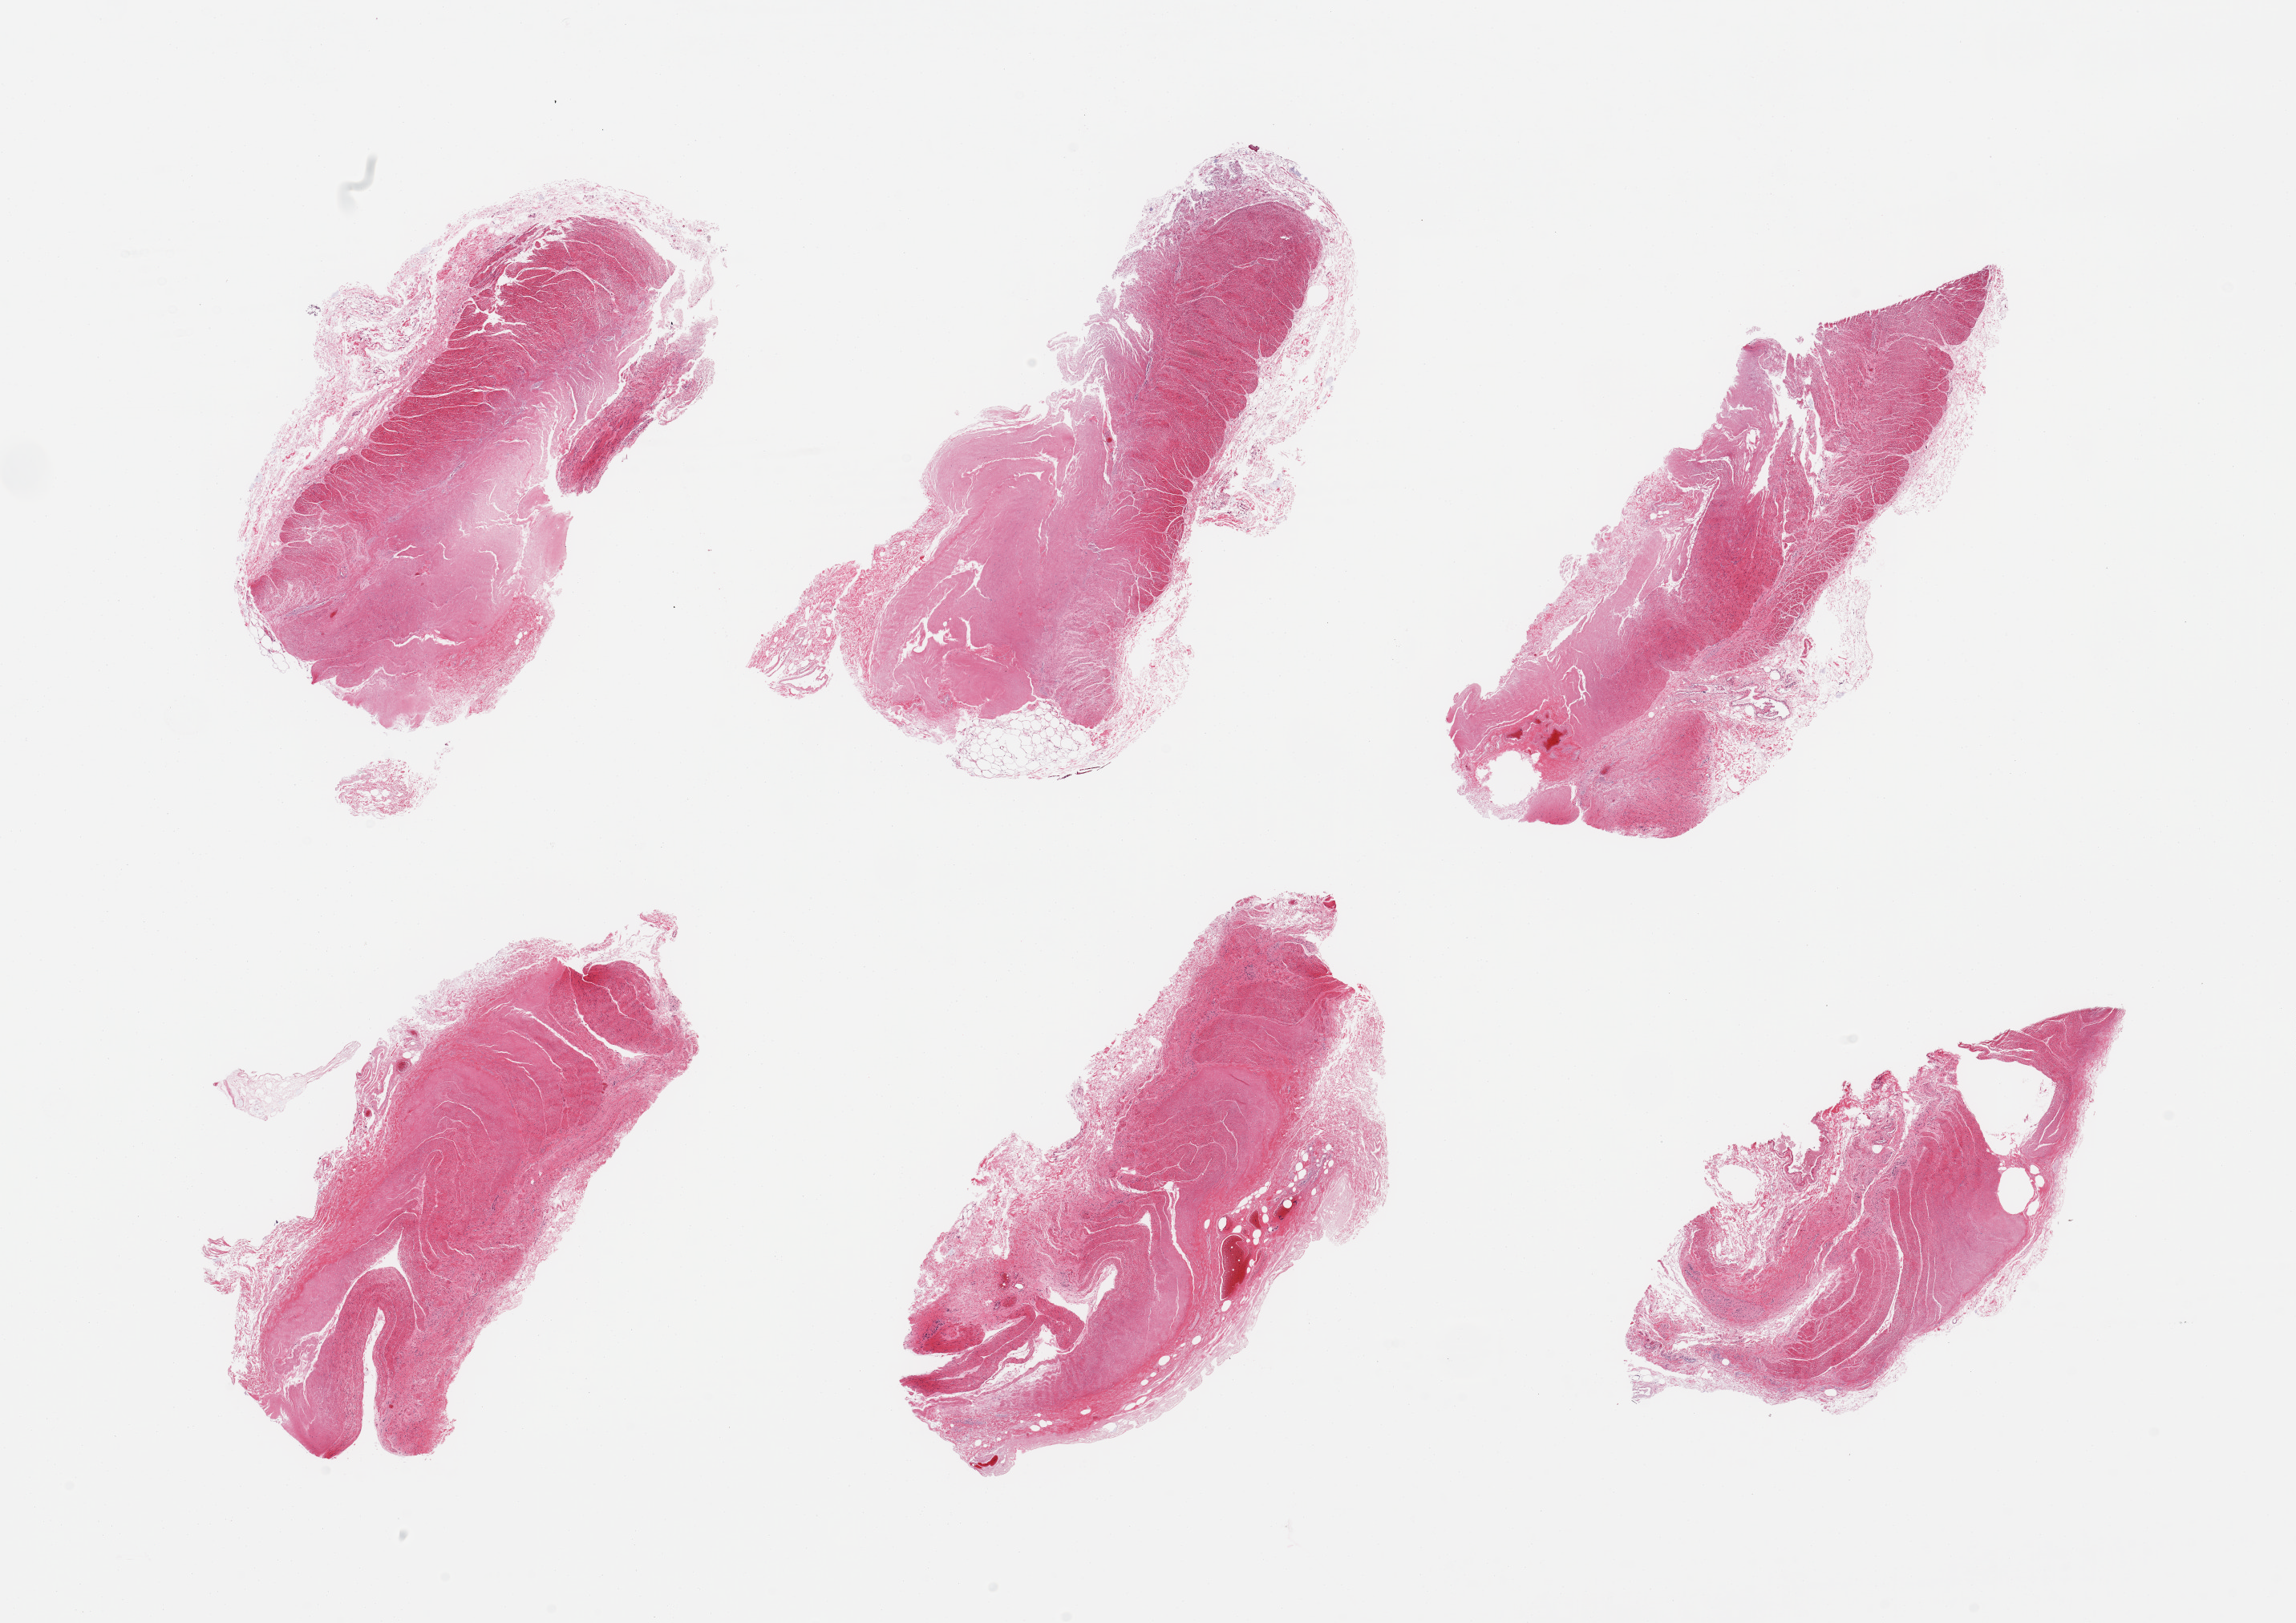
Digitized H&E-stained section — shown as a low-resolution overview of the whole scanned area (about 22.6 x 16.0 mm, from a 20x scan); PAXgene-fixed, paraffin-embedded tissue; section of sigmoid colon (target tissue); donor tissue sample.
Review note (as recorded): 6 pieces; autolyzed muscularis.